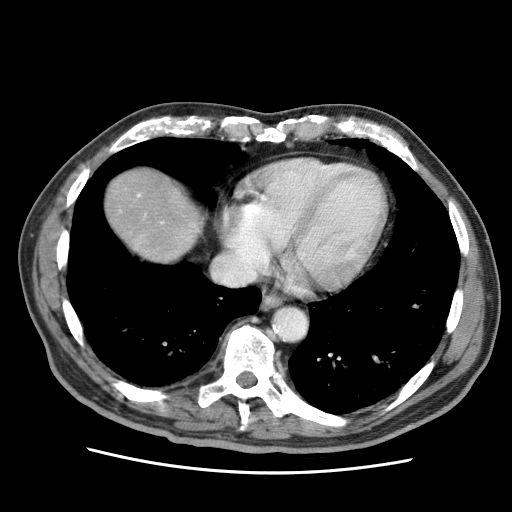
Contrast-enhanced abdominal CT (liver protocol), one axial slice; slice 64 of 75 in the series (ordered by position); 120 kVp; soft-tissue window (W 400 / L 40 HU); 2.5 mm slice thickness; 512 × 512 image matrix, field of view 360 × 360 mm. Case-level facts recorded for this patient, not image findings: diagnosis: hepatocellular carcinoma (patient treated with transarterial chemoembolisation; whether this scan precedes or follows treatment is not stated here); TNM stage (as recorded): Stage-IIIA; Child-Pugh class: A; tumour differentiation: well differentiated; tumour nodularity: multinodular.
Outlined on this slice (semi-automatically segmented with operator editing):
- liver parenchyma outside the tumour (the mass and vessels are separate outlines, so this box may not span the whole liver): bounding box (x1, y1, x2, y2) in pixels: (104, 168, 202, 262)
- liver vessels: (138, 194, 140, 197)